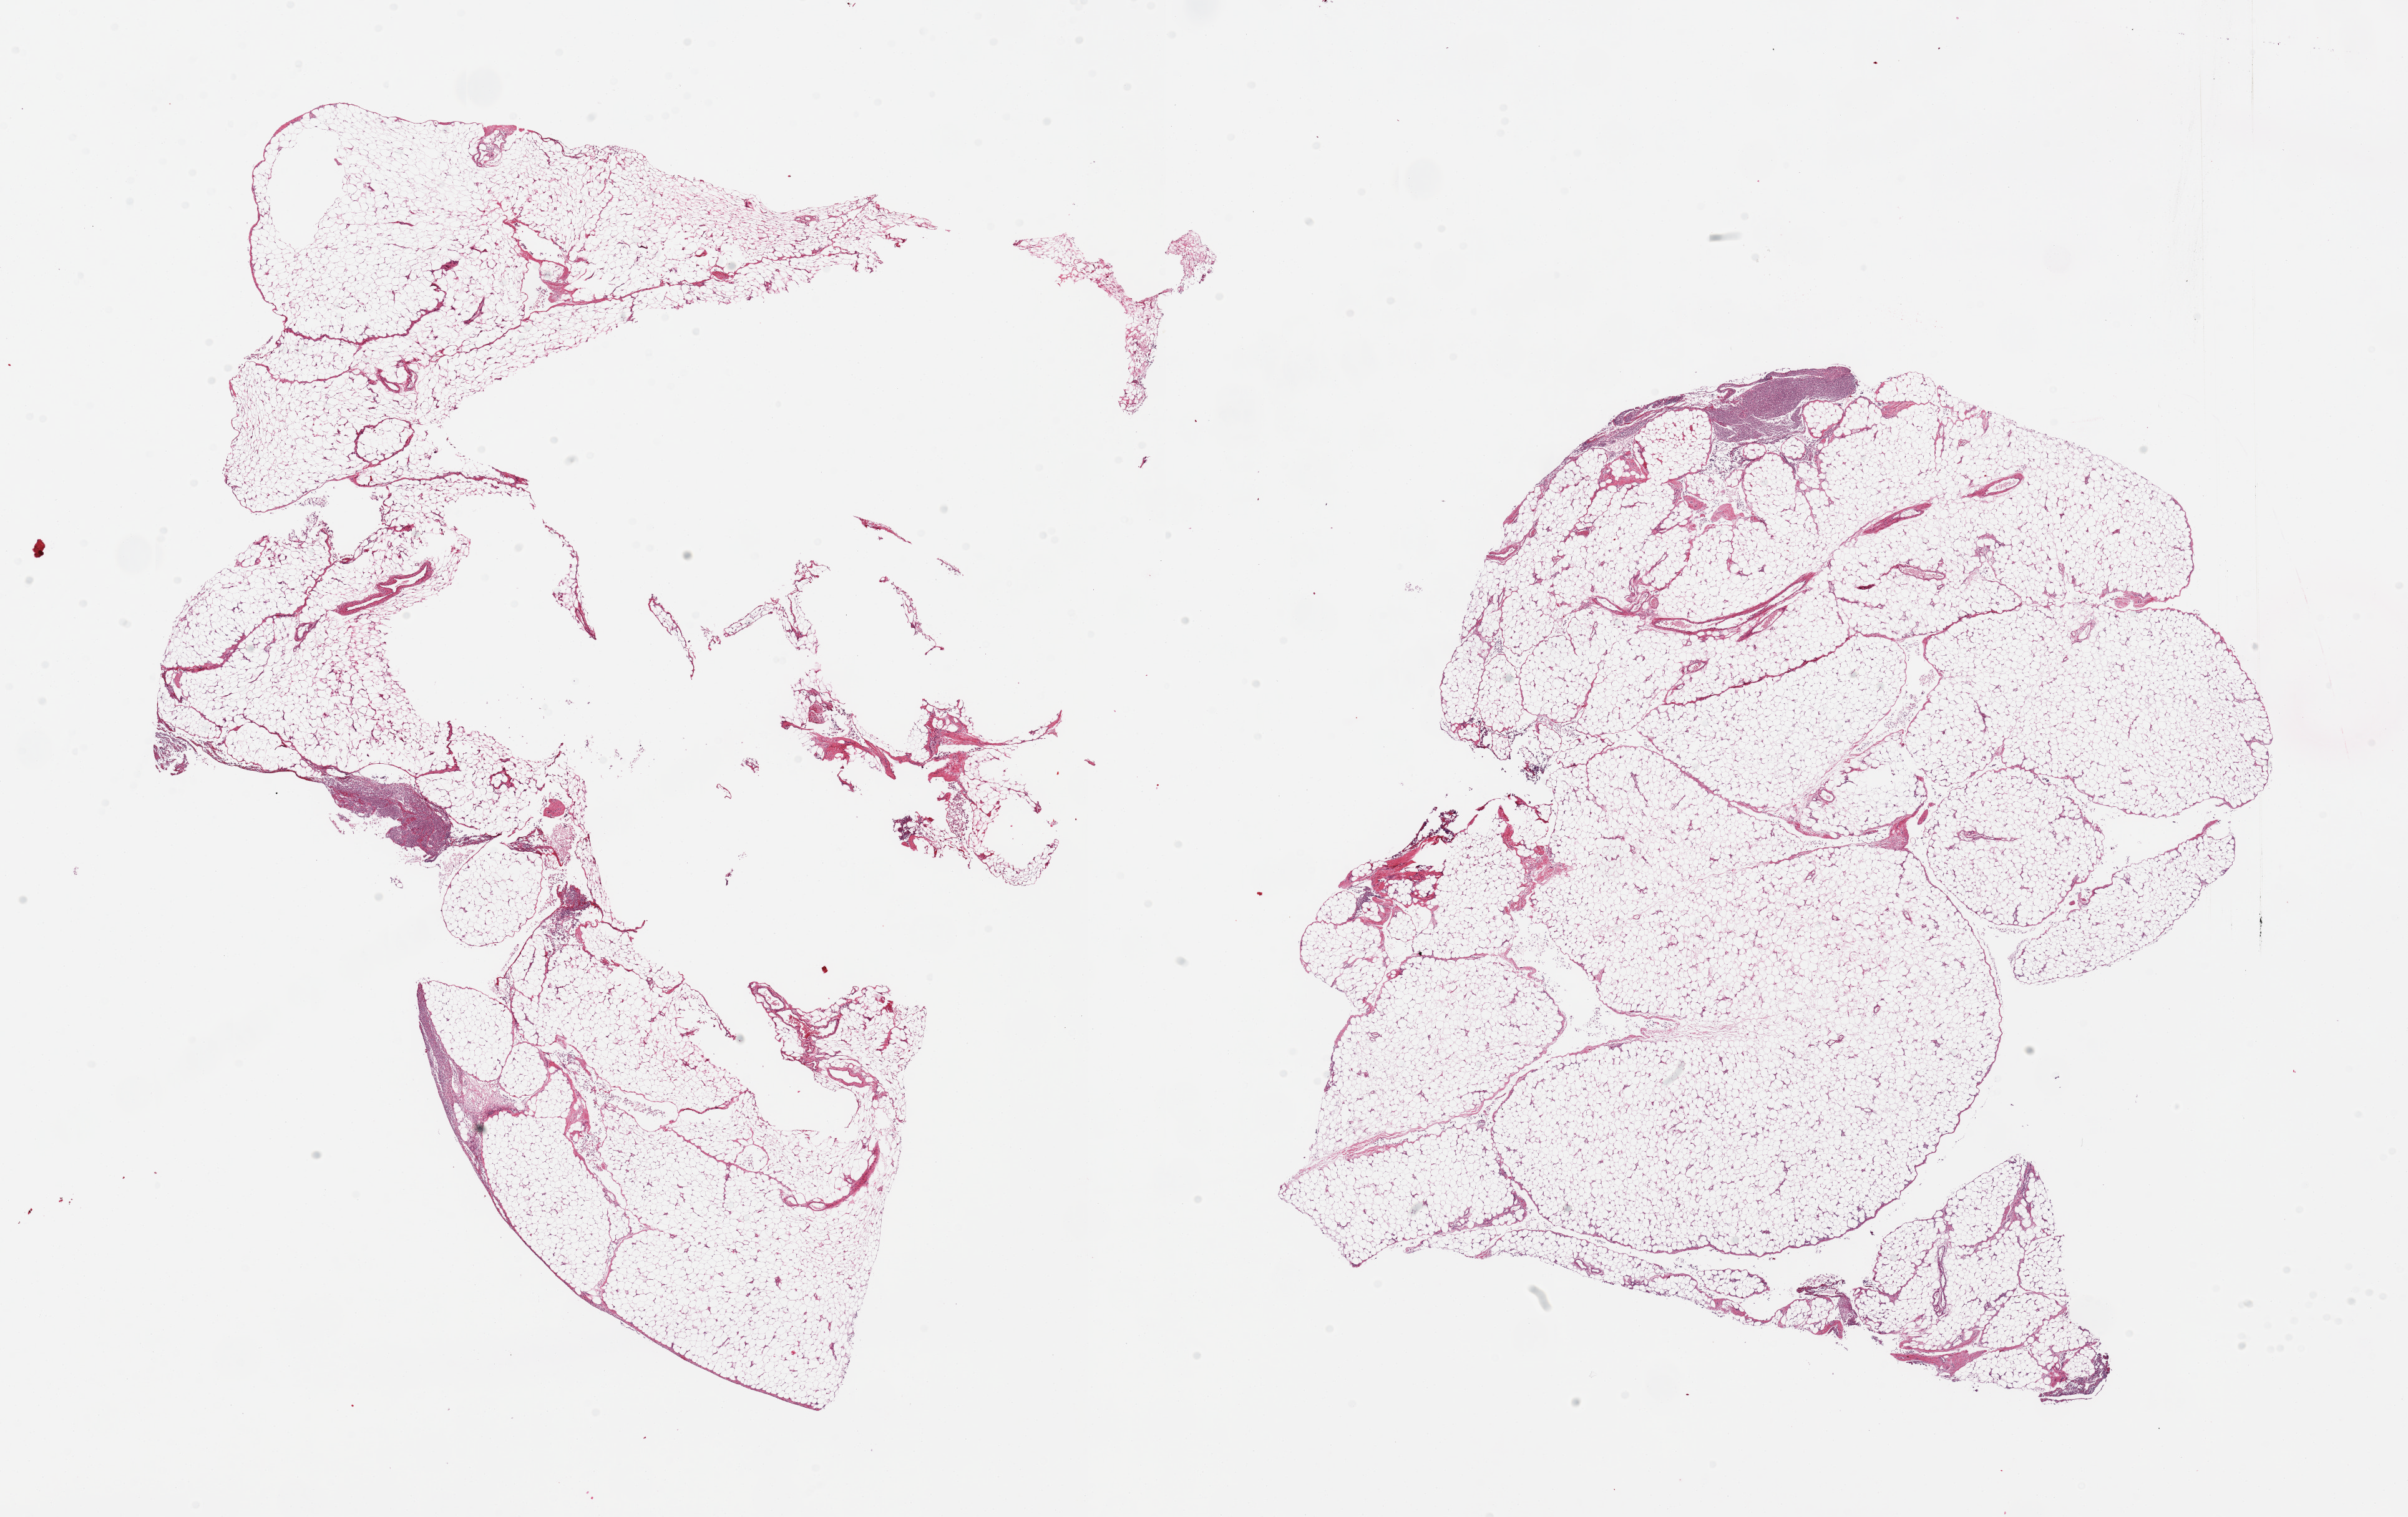
Hematoxylin and eosin (H&E) whole-slide image, brightfield — whole scanned area (about 30.5 x 19.2 mm) shown as a low-resolution overview, PAXgene-fixed, paraffin-embedded tissue, sampled site (target tissue): omentum, tissue donor sample. Male donor.
- pathologist's review note for this sample: 2 pieces; micro aggregates of polymorphonuclear leukocytes; vascular and fascia elements are ~5-10% of tissue